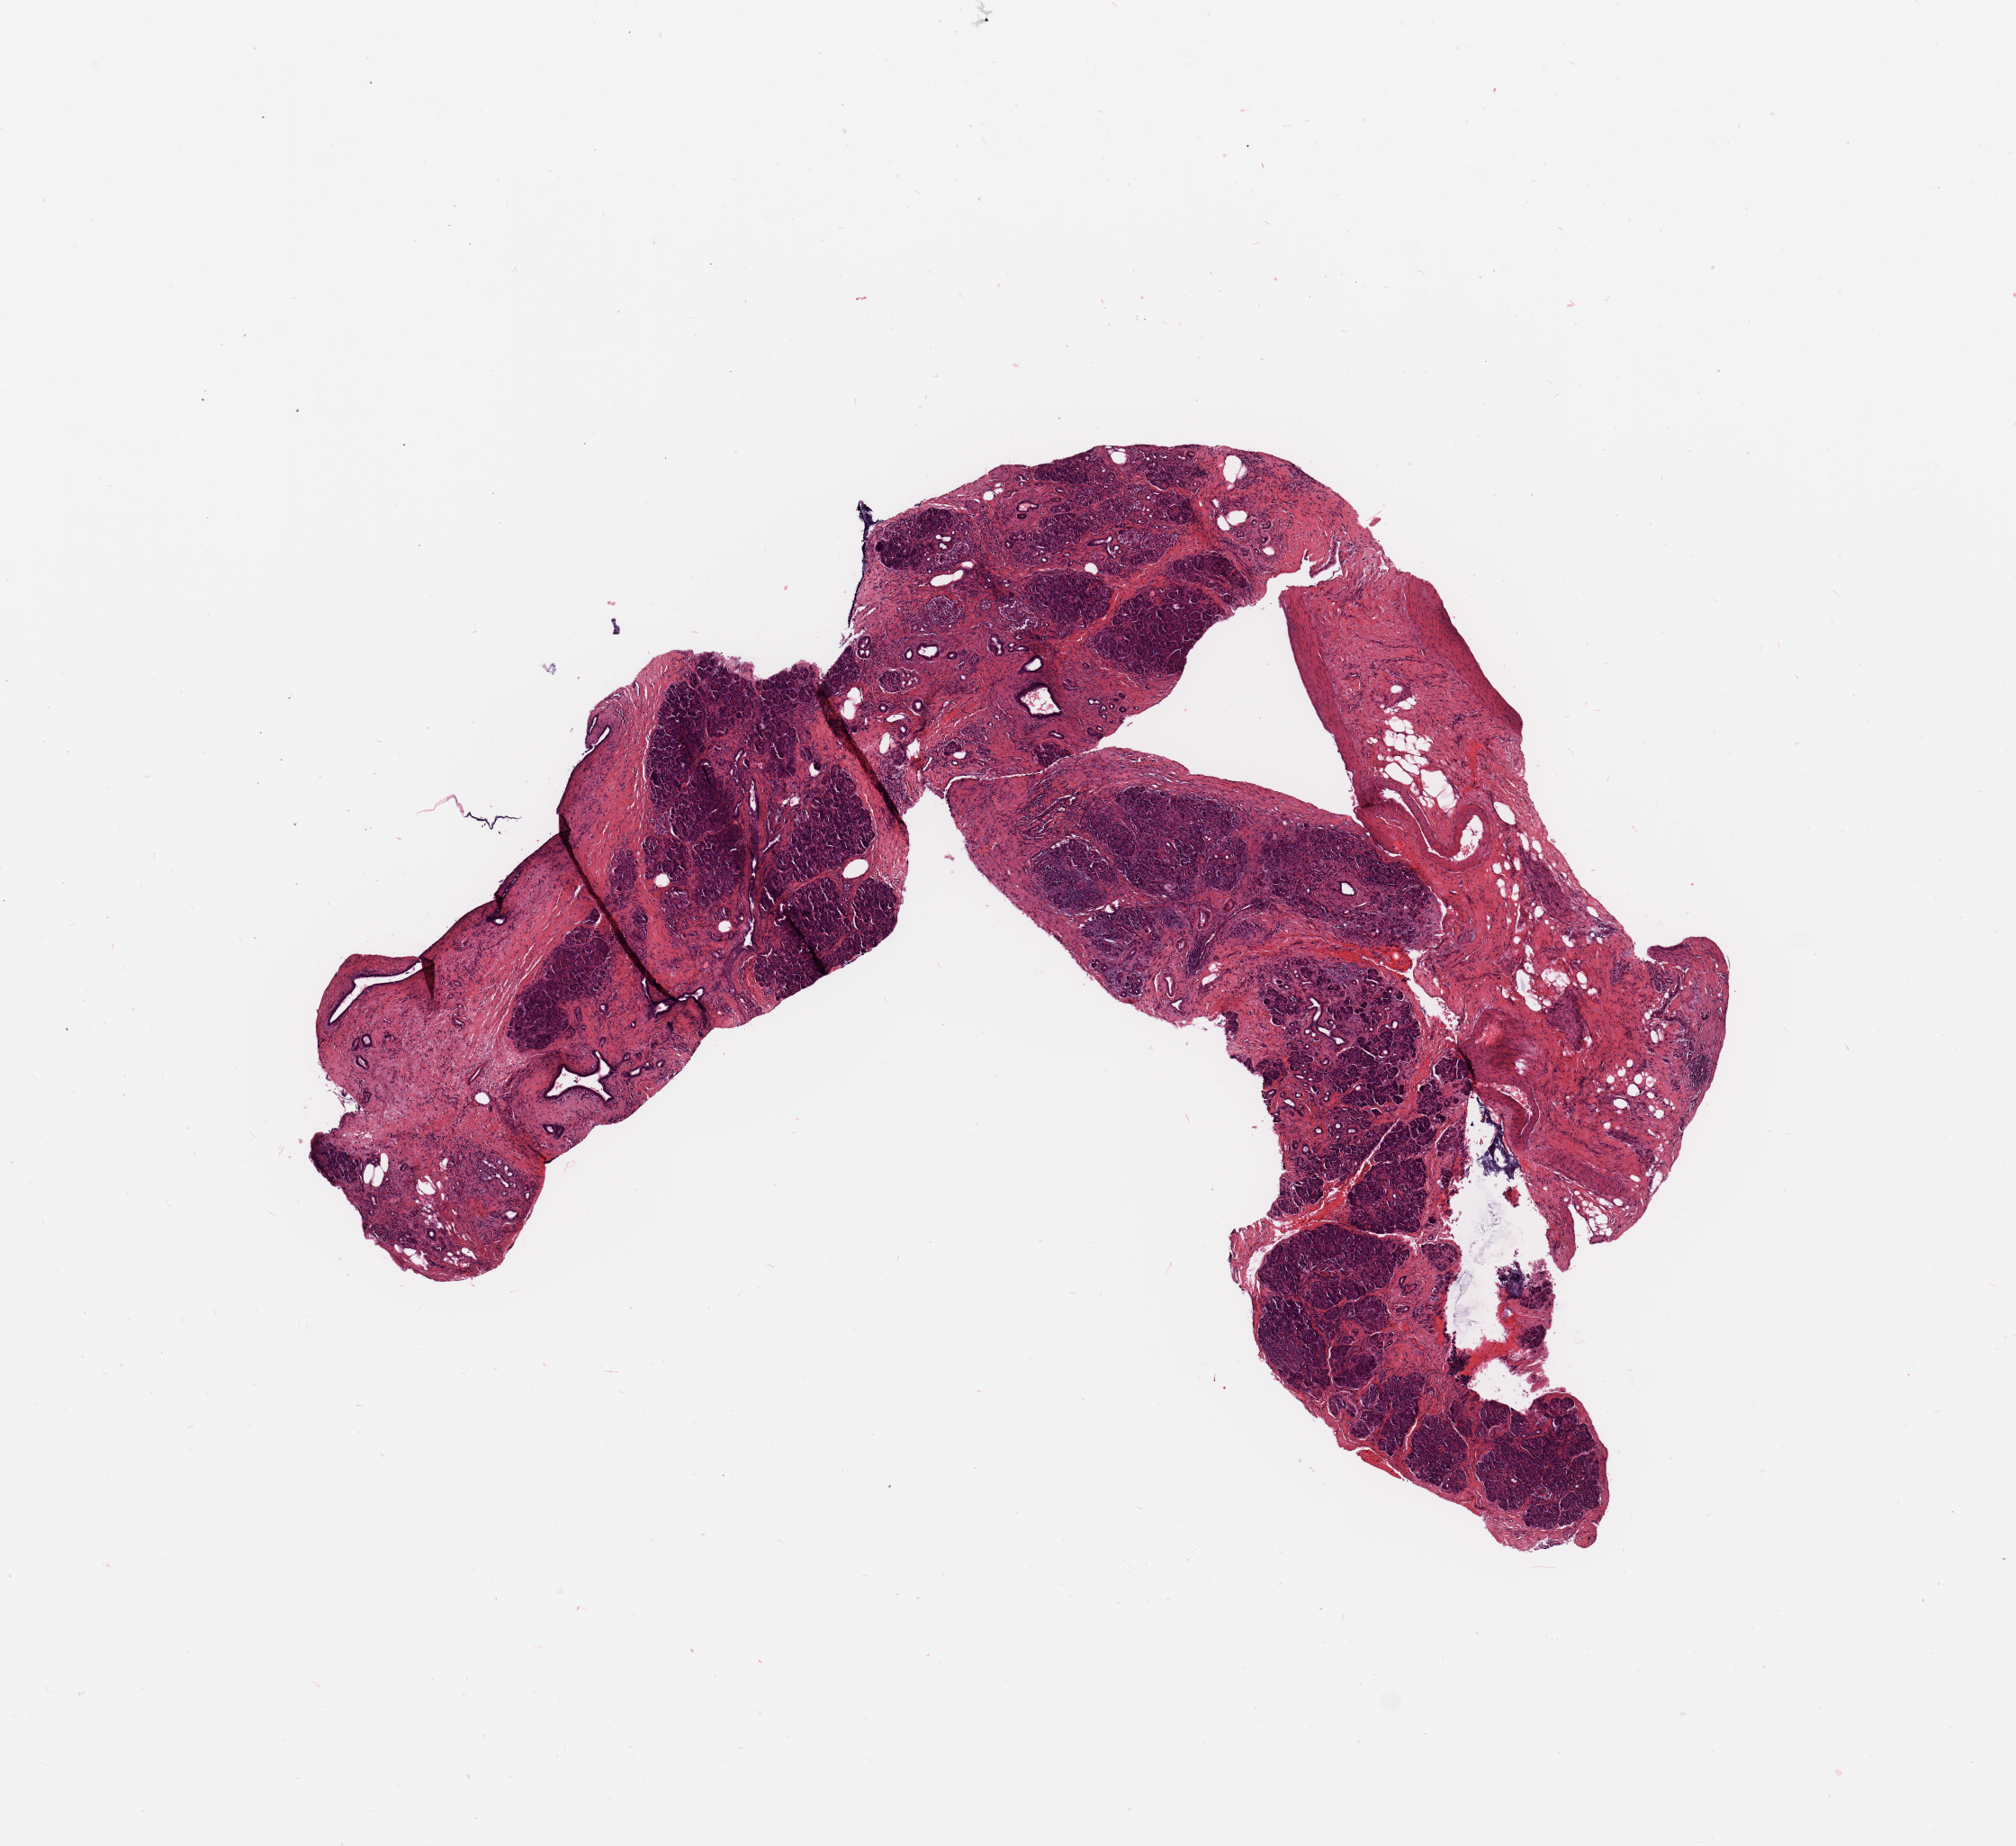
Whole-slide histology image, H&E-stained, whole scanned area (about 8.9 x 8.1 mm, acquisition: 20x scan) shown as a low-resolution overview. Tumour tissue sample, pancreas. Patient: male, age 66 years. Histologic grade: G3 (poorly differentiated).
Primary tumour site (as recorded): head. AJCC pathologic stage: IIA. Histologic diagnosis: Infiltrating duct carcinoma, NOS.